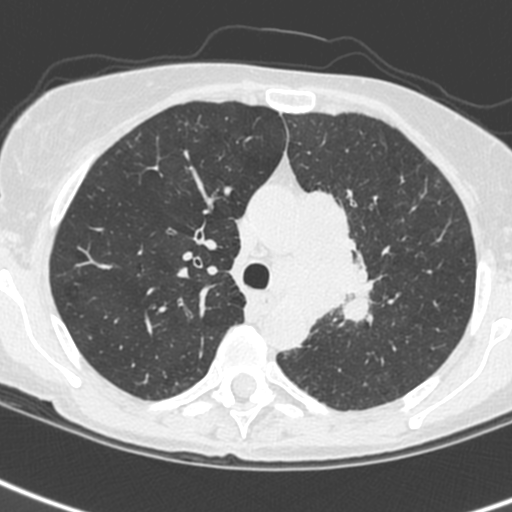
Low-dose screening chest CT, one axial slice. Slice 172 of 242 in the series (ordered by position). 120 kVp. Lung window (W 1500 / L -600 HU). 1.3 mm slice thickness. 512 × 512 image matrix.
Outlined on this slice (manually delineated by an expert):
- lesion 3 (tumor, upper lobe of left lung): box from (x=309, y=190) to (x=373, y=323) px